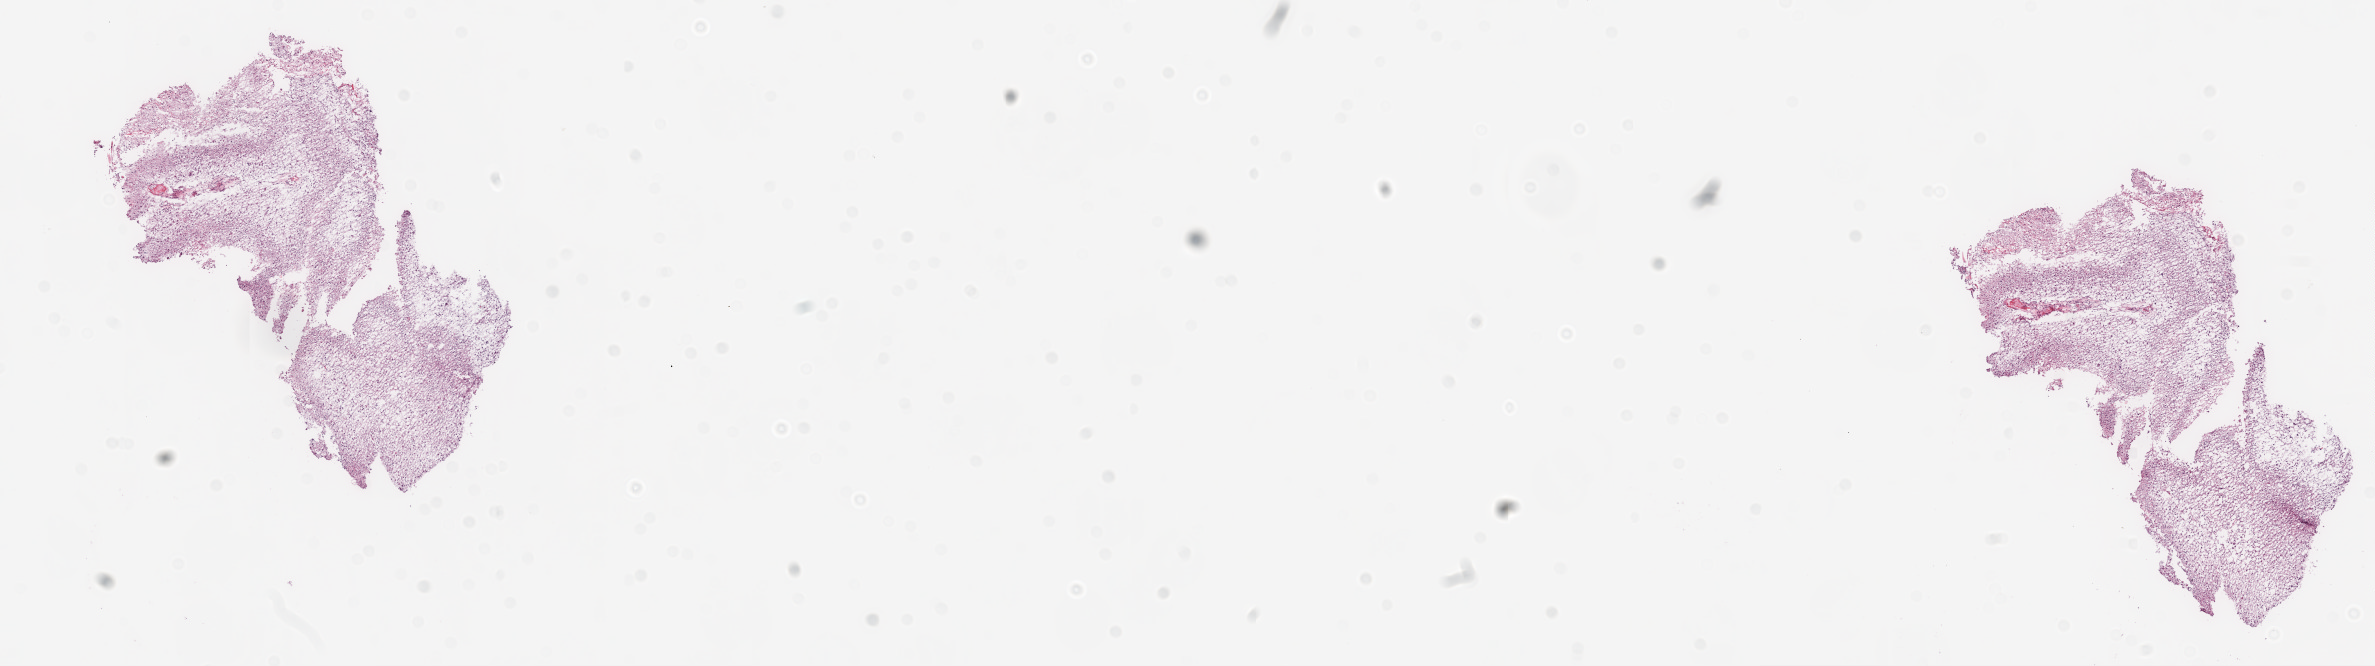
H&E-stained whole-slide image — a low-resolution overview of the entire scanned area, about 19.1 x 5.3 mm (from a 20x scan), frozen section, sample: primary tumour, brain. Male patient; age at initial diagnosis 56 years. Pathologist review of this section (percent, as recorded): tumour cells 95%, tumour nuclei 85%.
Histologic diagnosis: Glioblastoma.